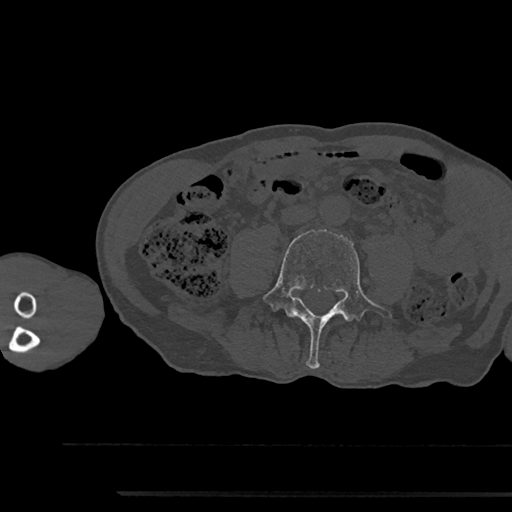
CT including the spine, one axial slice; slice 419 of 797 in the series (ordered by position); reconstruction kernel Br40s/3; 120 kVp; bone window (W 1800 / L 400 HU); 512 × 512 image matrix, field of view 367 × 367 mm. Patient: male, 79 years. Case-level facts recorded for this patient, not image findings: primary cancer: prostate.
Outlined on this slice (semi-automatic segmentation, software-assisted and operator-edited):
- L4 vertebra: box from (x=262, y=230) to (x=392, y=369) px